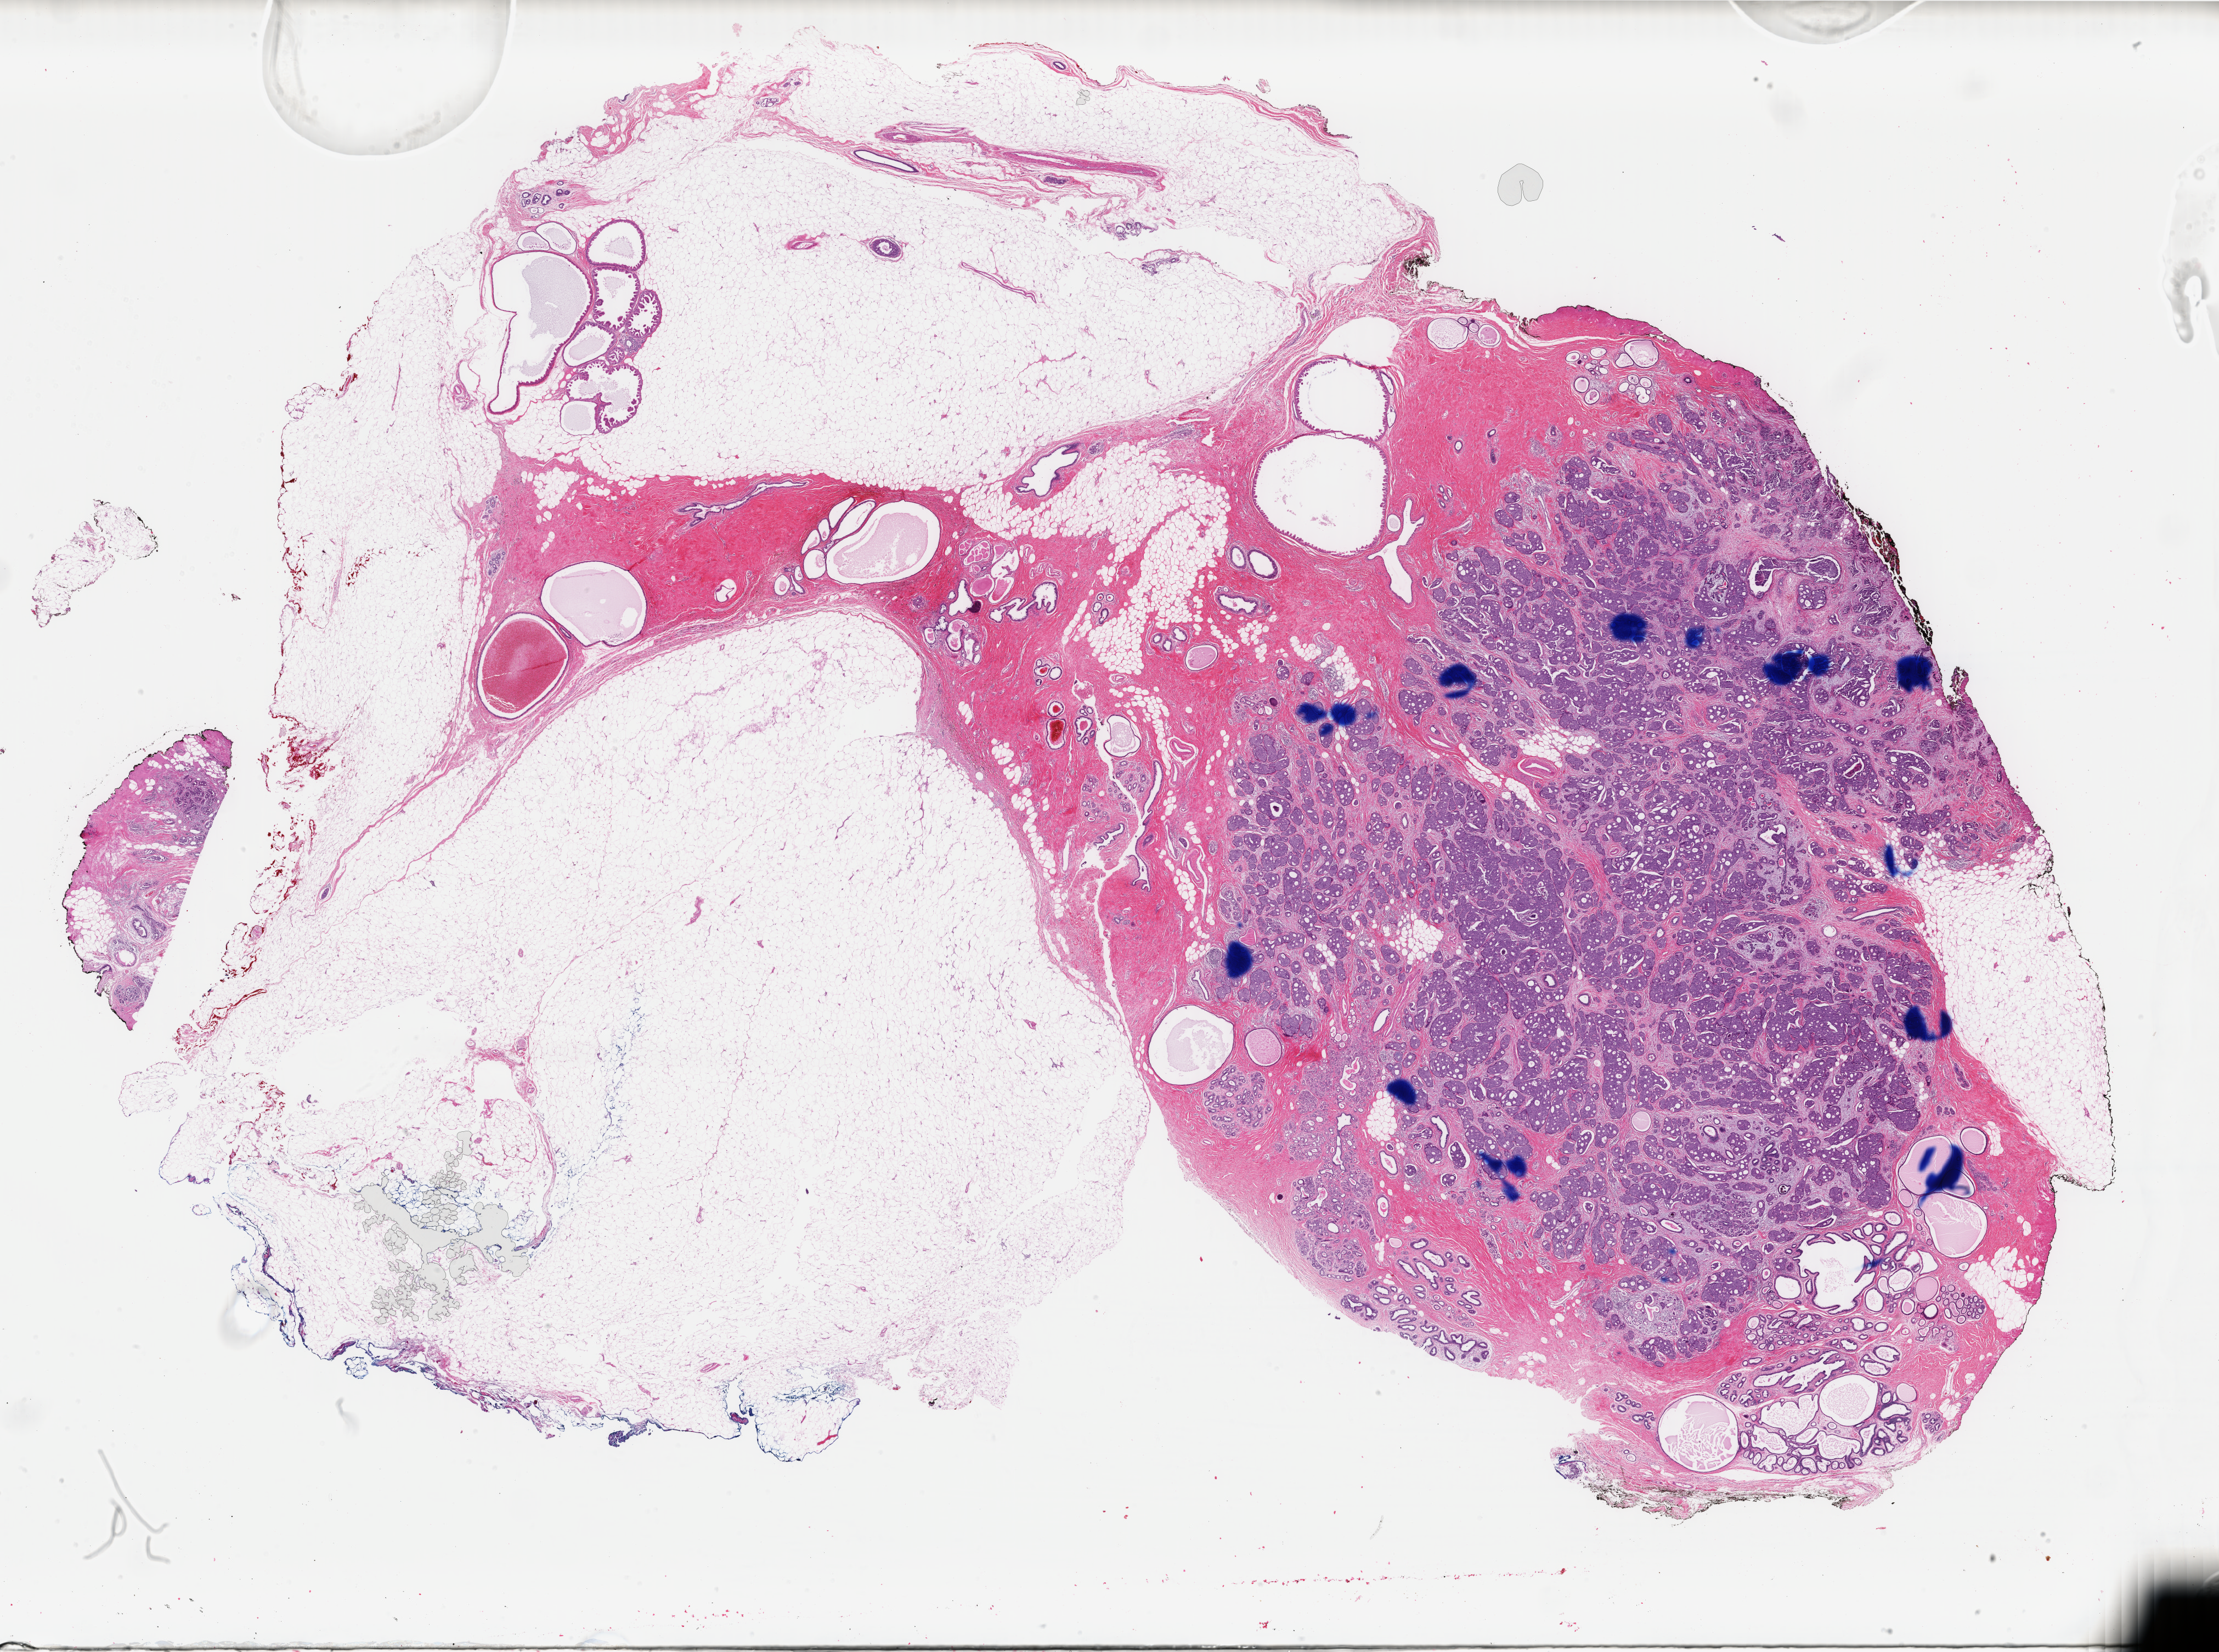
Digitized Hematoxylin and eosin (H&E) stained tissue section (whole slide) — low-resolution overview of the scanned area, about 32.1 x 23.9 mm. FFPE section. Sample: primary tumour, breast. Female patient; age at initial diagnosis 54 years.
AJCC pathologic stage: I (4th edition). Pathologic diagnosis: Cribriform carcinoma, NOS.